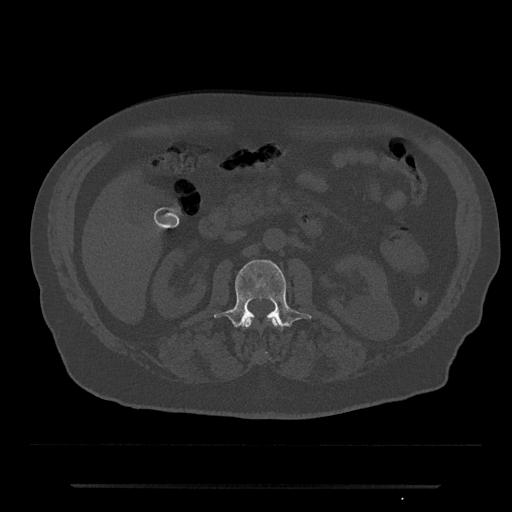
CT including the spine, one axial slice; slice 484 of 797 in the series (ordered by position); reconstruction kernel Br40s/3; bone window (W 1800 / L 400 HU); 0.5 mm slice thickness; 512 × 512 image matrix, field of view 434 × 434 mm. Male patient, age 80 years. From the clinical record (not read from this slice): primary cancer: prostate; vertebrae with lytic lesions (as recorded): L1, T11.
Outlined on this slice (semi-automatically segmented with operator editing):
- L1 vertebra: box from (x=243, y=318) to (x=280, y=328) px
- L2 vertebra: (x=214, y=260)–(x=312, y=328)